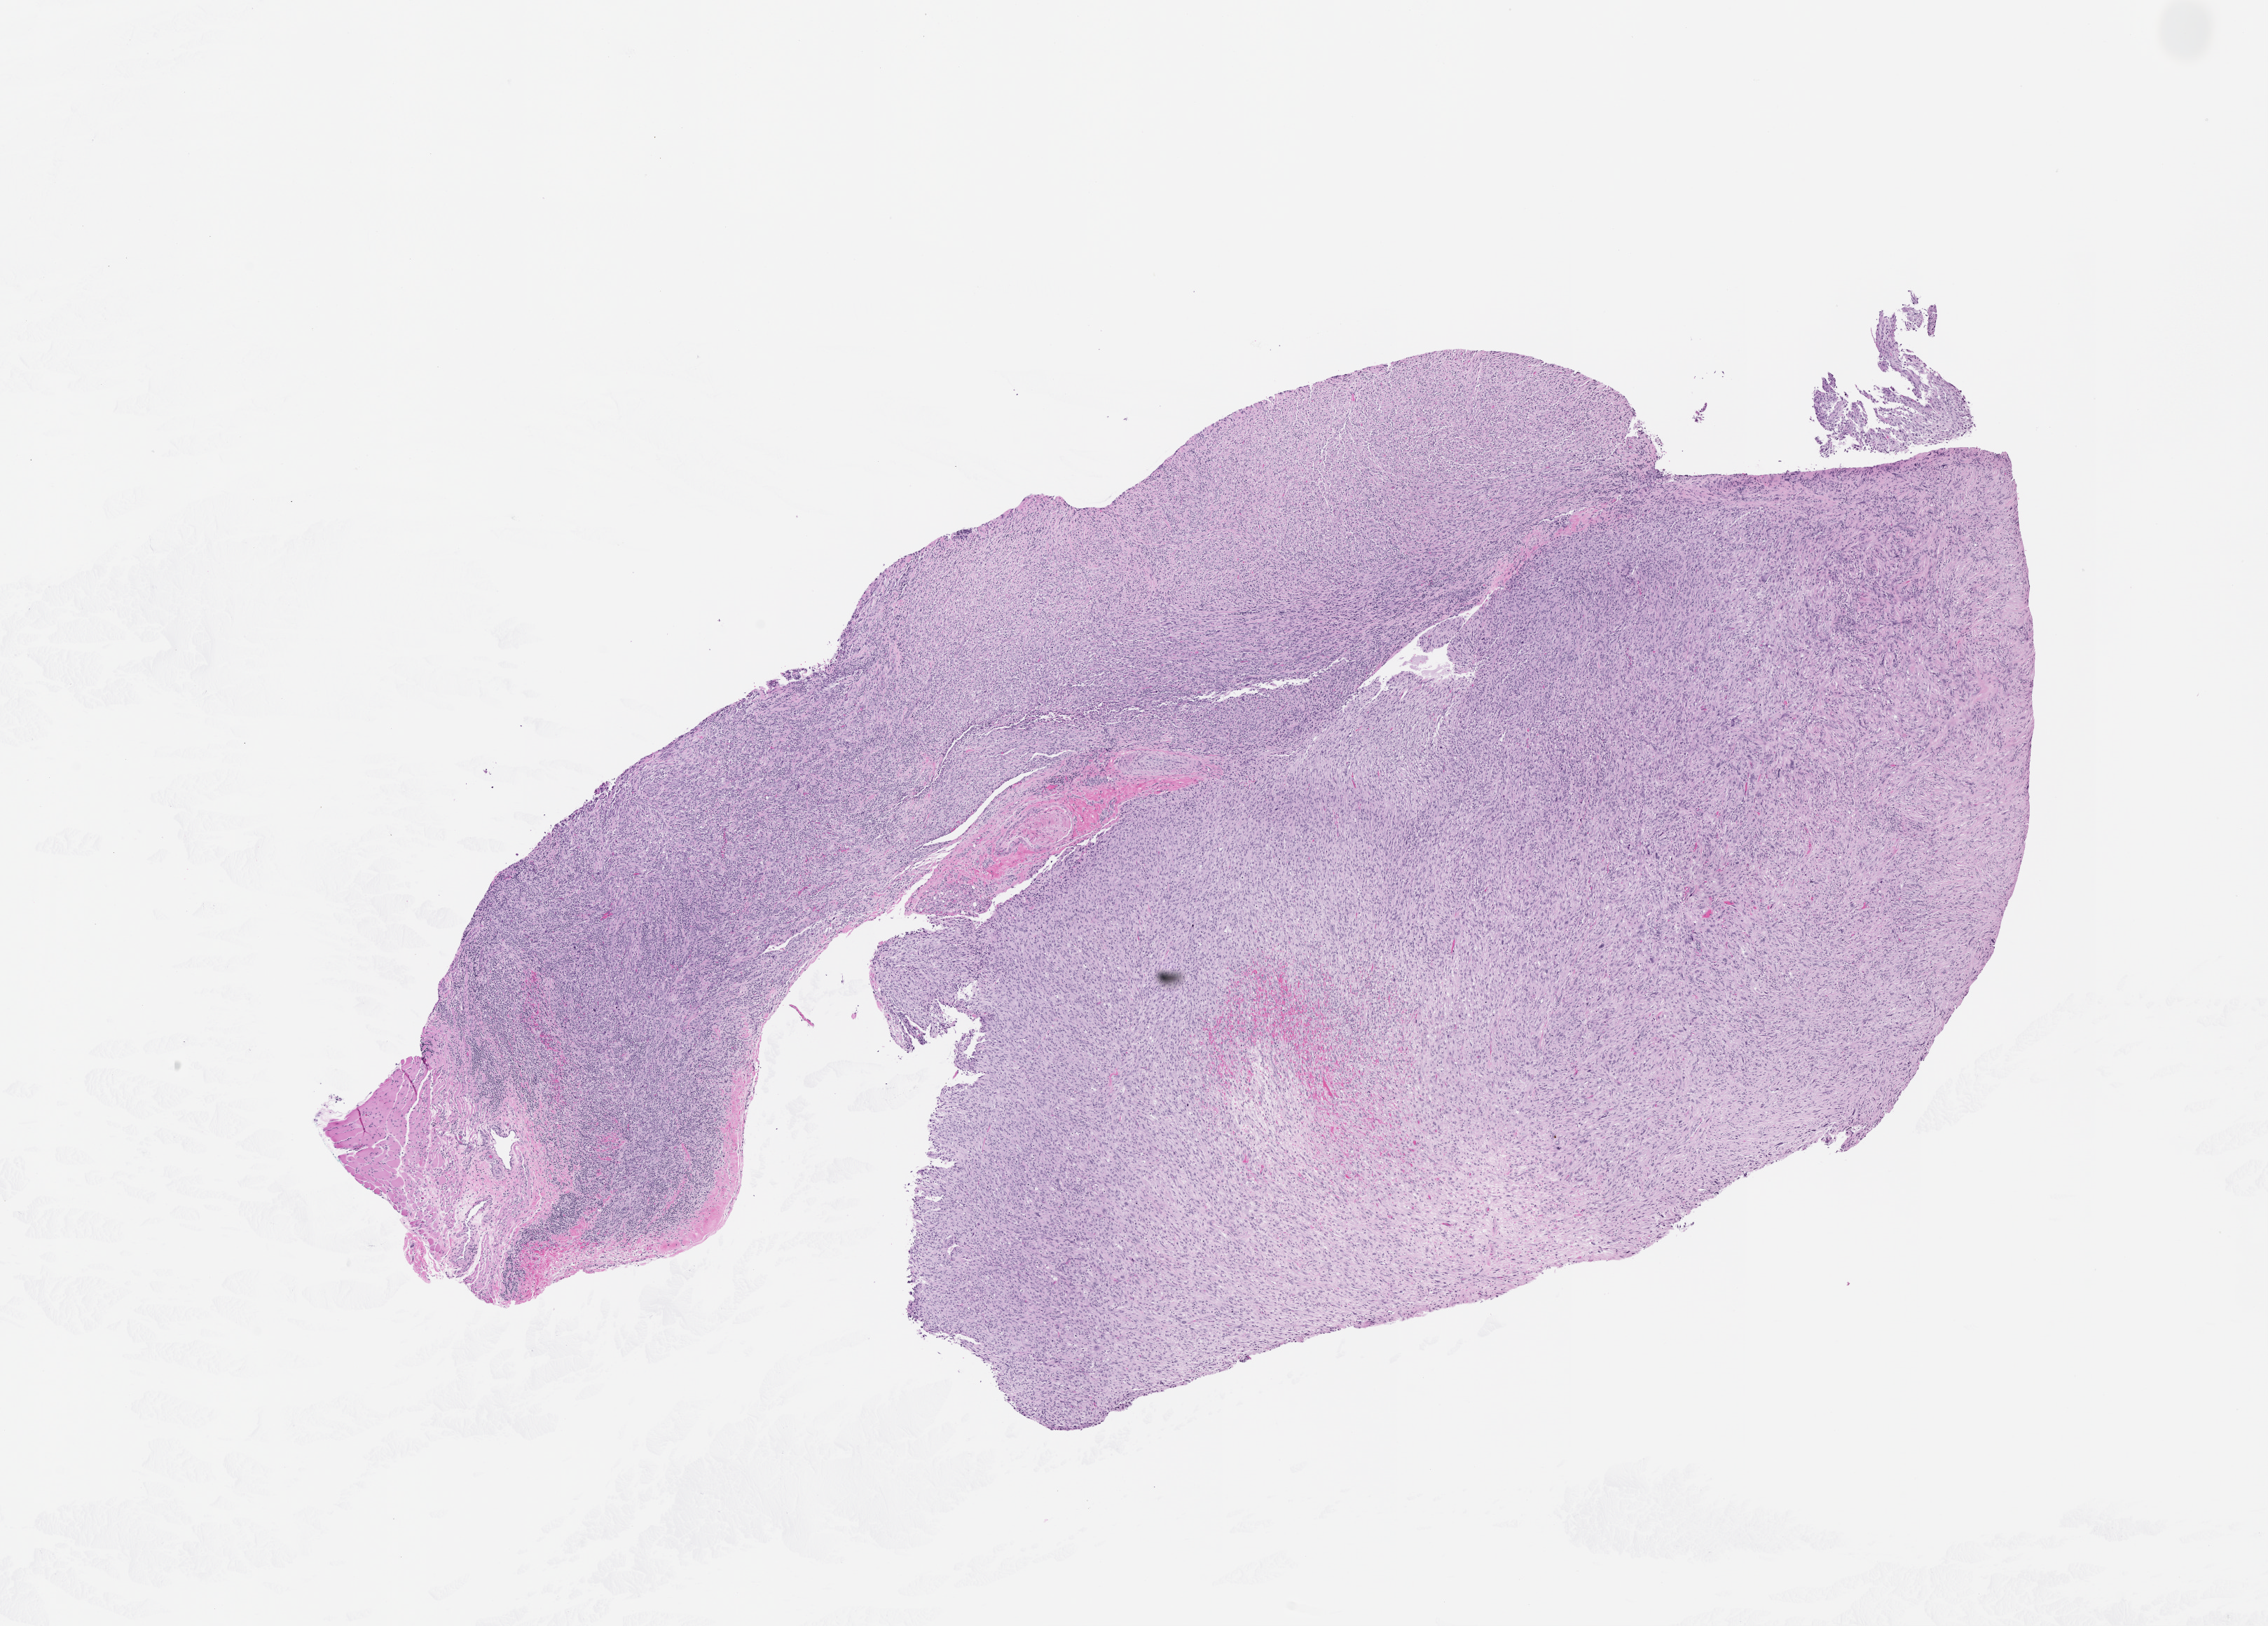
Whole-slide histology image, Hematoxylin and eosin (H&E) stained — whole scanned area (about 13.0 x 9.3 mm, slide scanned at 20x) shown as a low-resolution overview.
* patient diagnosis (cohort enrolment): sarcoma (site not recorded at cohort level)